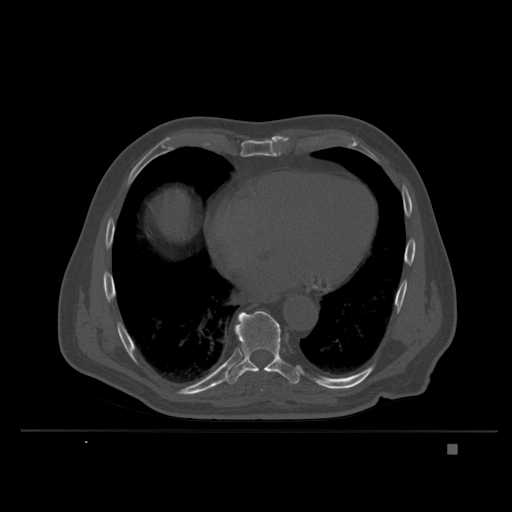
CT including the spine, one axial slice; slice 216 of 435 in the series (ordered by position); bone window (W 1800 / L 400 HU); 1.5 mm slice thickness; 512 × 512 image matrix, field of view 434 × 434 mm. Male patient, age 73 years. From the clinical record (not read from this slice): primary cancer: skin.
Structures marked on this image (semi-automatically segmented with operator editing):
- T9 vertebra: bounding box <225,311,300,385> (left, top, right, bottom; pixels)